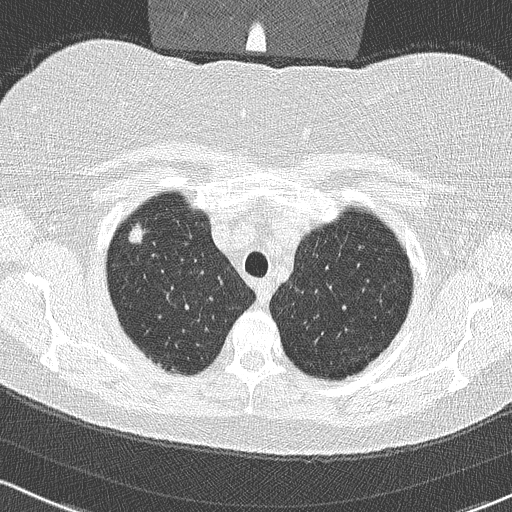
Low-dose screening chest CT, one axial slice; slice 269 of 315 in the series (ordered by position); 120 kVp; lung window (W 1500 / L -600 HU); 2 mm slice thickness; 512 × 512 image matrix, field of view 320 × 320 mm.
Outlined on this slice (manually delineated by an expert):
- lesion 1 (tumor, upper lobe of right lung): bounding box [x1, y1, x2, y2] px = [129, 224, 143, 244]